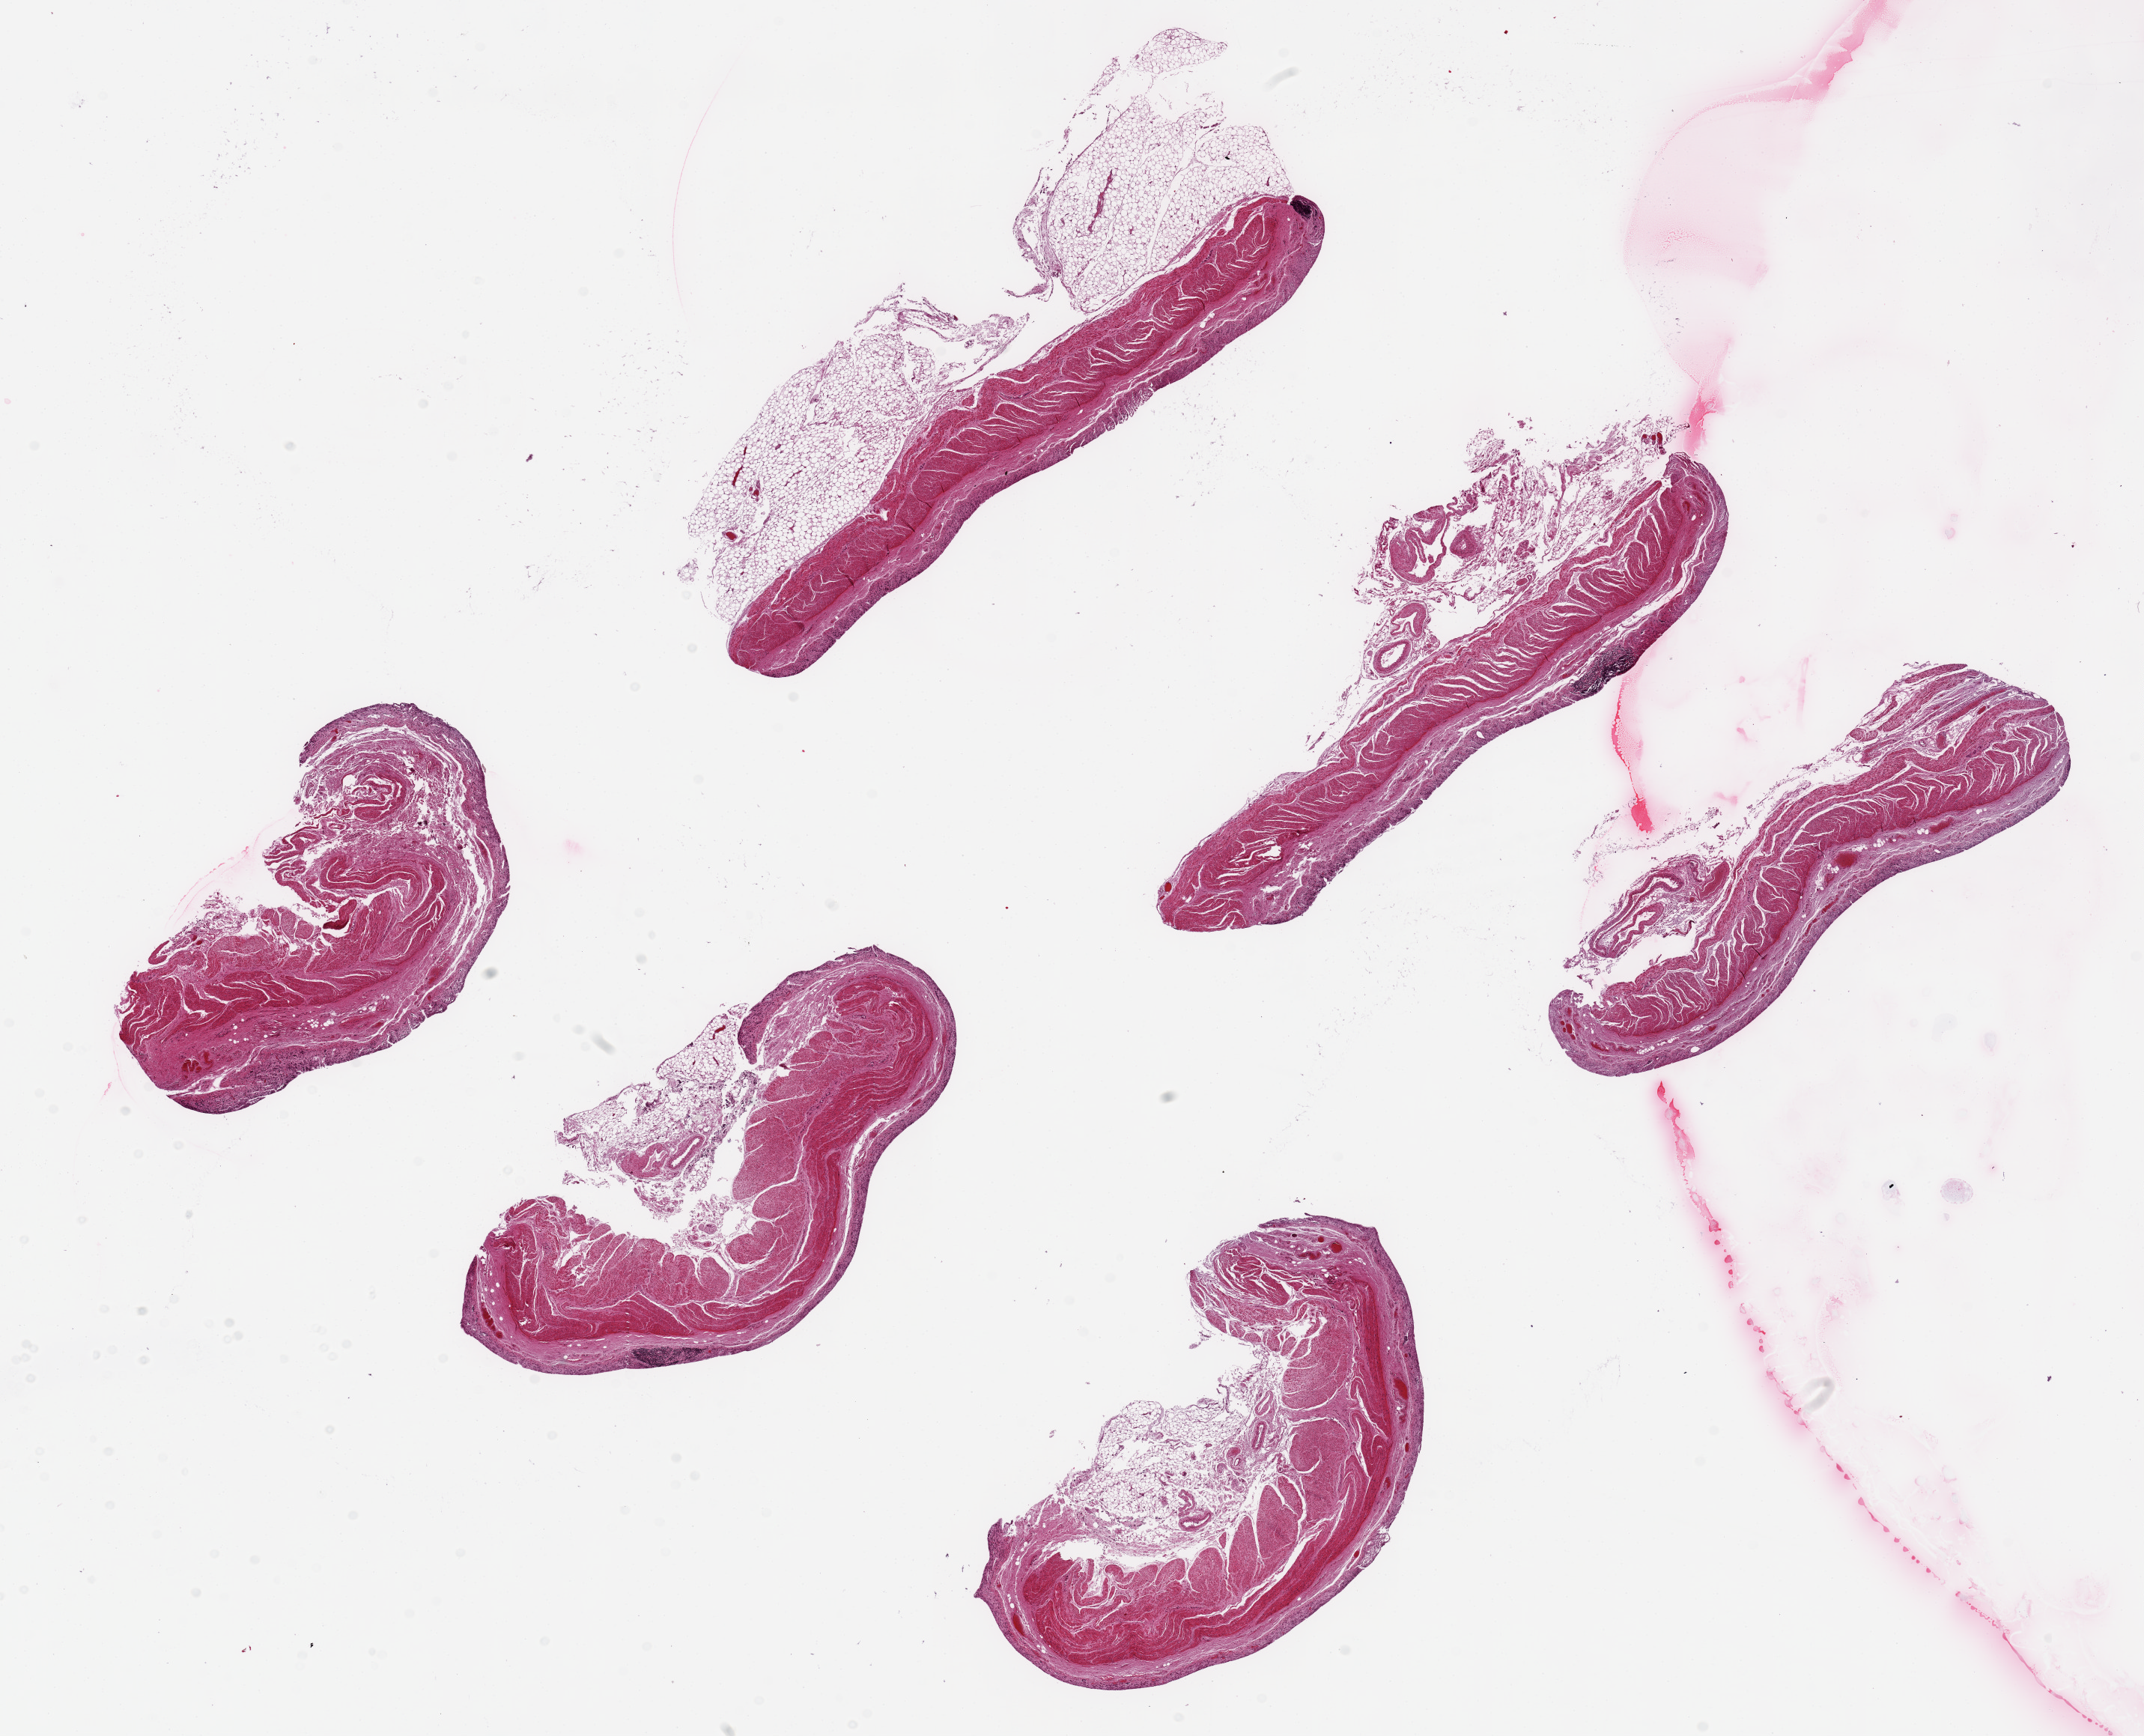
Whole-slide image, haematoxylin and eosin stain, low-resolution overview of the scanned area, about 22.6 x 18.3 mm. PAXgene-fixed paraffin-embedded (PFPE) section. Target tissue: transverse colon. Tissue donor sample. Female donor.
Reviewer comment on this tissue sample: 6 ~8x2mm pieces. Mucosa totally autolyzed, many have adherent fat/fibrovascular tissue fragments.